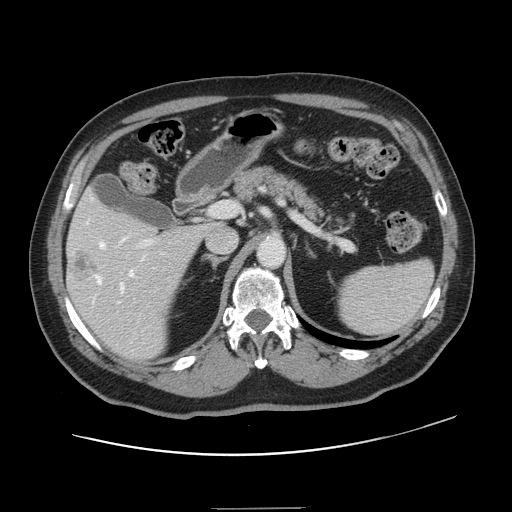
Contrast-enhanced abdominal CT, one axial slice. 120 kVp. Intravenous contrast given. Soft-tissue window (W 400 / L 40 HU). 2.5 mm slice thickness. 512 × 512 image matrix, field of view 402 × 402 mm. Male patient, age 62 years. From the clinical record (not read from this slice): diagnosis: colorectal cancer liver metastases, imaged before liver resection; multiple liver metastases: yes.
Annotated regions visible in this slice (expert manual segmentation):
- hepatic veins: bounding box (x1, y1, x2, y2) in pixels: (93, 243, 144, 301)
- liver: (67, 193, 209, 361)
- planned liver remnant (the part of the liver to remain after resection): (70, 193, 213, 237)
- portal vein (with intrahepatic branches): (118, 205, 220, 304)
- liver metastasis: (71, 253, 99, 281)